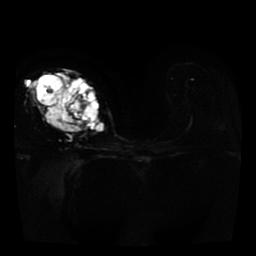
Breast MRI, one axial slice; position 24 of 41 along the scan axis; diffusion-weighted series; image 2 of 4 stored at this slice position (different b-values; order by instance number); 1.5 T; 256 × 256 image matrix. Female patient.
Annotated regions visible in this slice (outlined manually by an expert reader):
- tumour on diffusion-weighted imaging: bounding box [x1, y1, x2, y2] px = [47, 73, 104, 131]